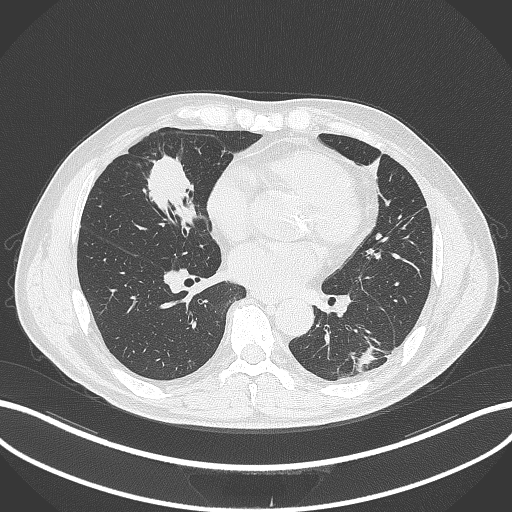
Chest CT, one axial slice; 120 kVp; lung window (W 1500 / L -600 HU); 1 mm slice thickness; 512 × 512 image matrix. Patient: male, 59 years. From the clinical record (not read from this slice): clinical TNM (as recorded): T2a N1 M0.
Annotated regions visible in this slice (bounding box drawn by a radiologist):
- lung tumour (recorded histology: adenocarcinoma): bounding box <137,153,202,236> (left, top, right, bottom; pixels)